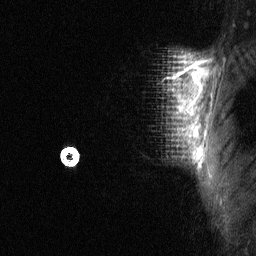
Breast MRI (dynamic contrast-enhanced), one sagittal slice. Position 52 of 64 along the scan axis. Dynamic contrast-enhanced study with each time point stored as its own series, time point 2 of 3 at this slice position (early post-contrast, ordered by acquisition time). 1.5 T. TE 4.8 ms, TR 27 ms. 2 mm slice thickness. 256 × 256 image matrix. Female patient, age 36 years. Case-level facts recorded for this patient, not image findings: setting: breast cancer imaged before/during neoadjuvant chemotherapy; receptor status: HR-positive, HER2-negative.
Annotated regions visible in this slice (semi-automatic segmentation, software-assisted and operator-edited):
- analysis volume of interest (the breast-tissue region the enhancement analysis was run in; not a lesion): box from (x=67, y=51) to (x=214, y=169) px
- tumour enhancement mask (voxels above the 90 % enhancement threshold inside the analysis volume of interest): (x=191, y=63)–(x=202, y=159)